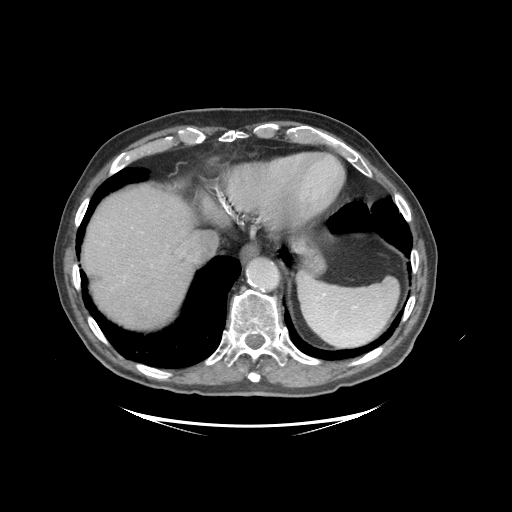
Contrast-enhanced abdominal CT (liver protocol), one axial slice; position 83 of 99 along the scan axis; reconstruction kernel STANDARD; soft-tissue window (W 400 / L 40 HU); 2.5 mm slice thickness; 512 × 512 image matrix. Case-level facts recorded for this patient, not image findings: diagnosis: hepatocellular carcinoma (patient treated with transarterial chemoembolisation; whether this scan precedes or follows treatment is not stated here); TNM stage (as recorded): Stage-I; Child-Pugh class: A; tumour differentiation: moderately differentiated.
Structures marked on this image (semi-automatically segmented with operator editing):
- liver parenchyma outside the tumour (the mass and vessels are separate outlines, so this box may not span the whole liver): bounding box [x1, y1, x2, y2] px = [82, 186, 216, 328]